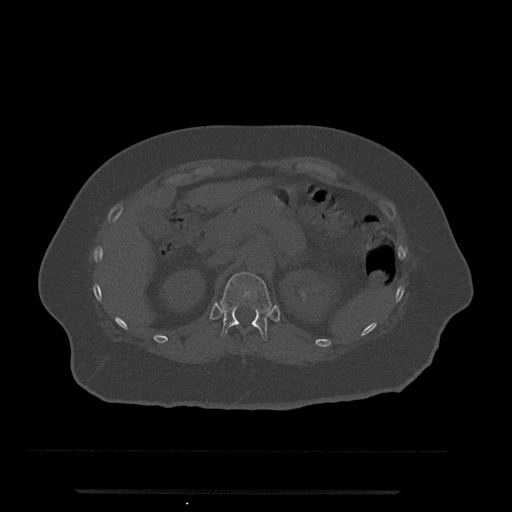
CT including the spine, one axial slice; slice 179 of 797 in the series (ordered by position); 120 kVp; bone window (W 1800 / L 400 HU); 512 × 512 image matrix, field of view 440 × 440 mm. Patient: female, 51 years. From the clinical record (not read from this slice): primary cancer: neuro; vertebrae with lytic lesions (as recorded): T8.
Outlined on this slice (semi-automatic segmentation, software-assisted and operator-edited):
- T12 vertebra: box from (x=221, y=272) to (x=272, y=341) px